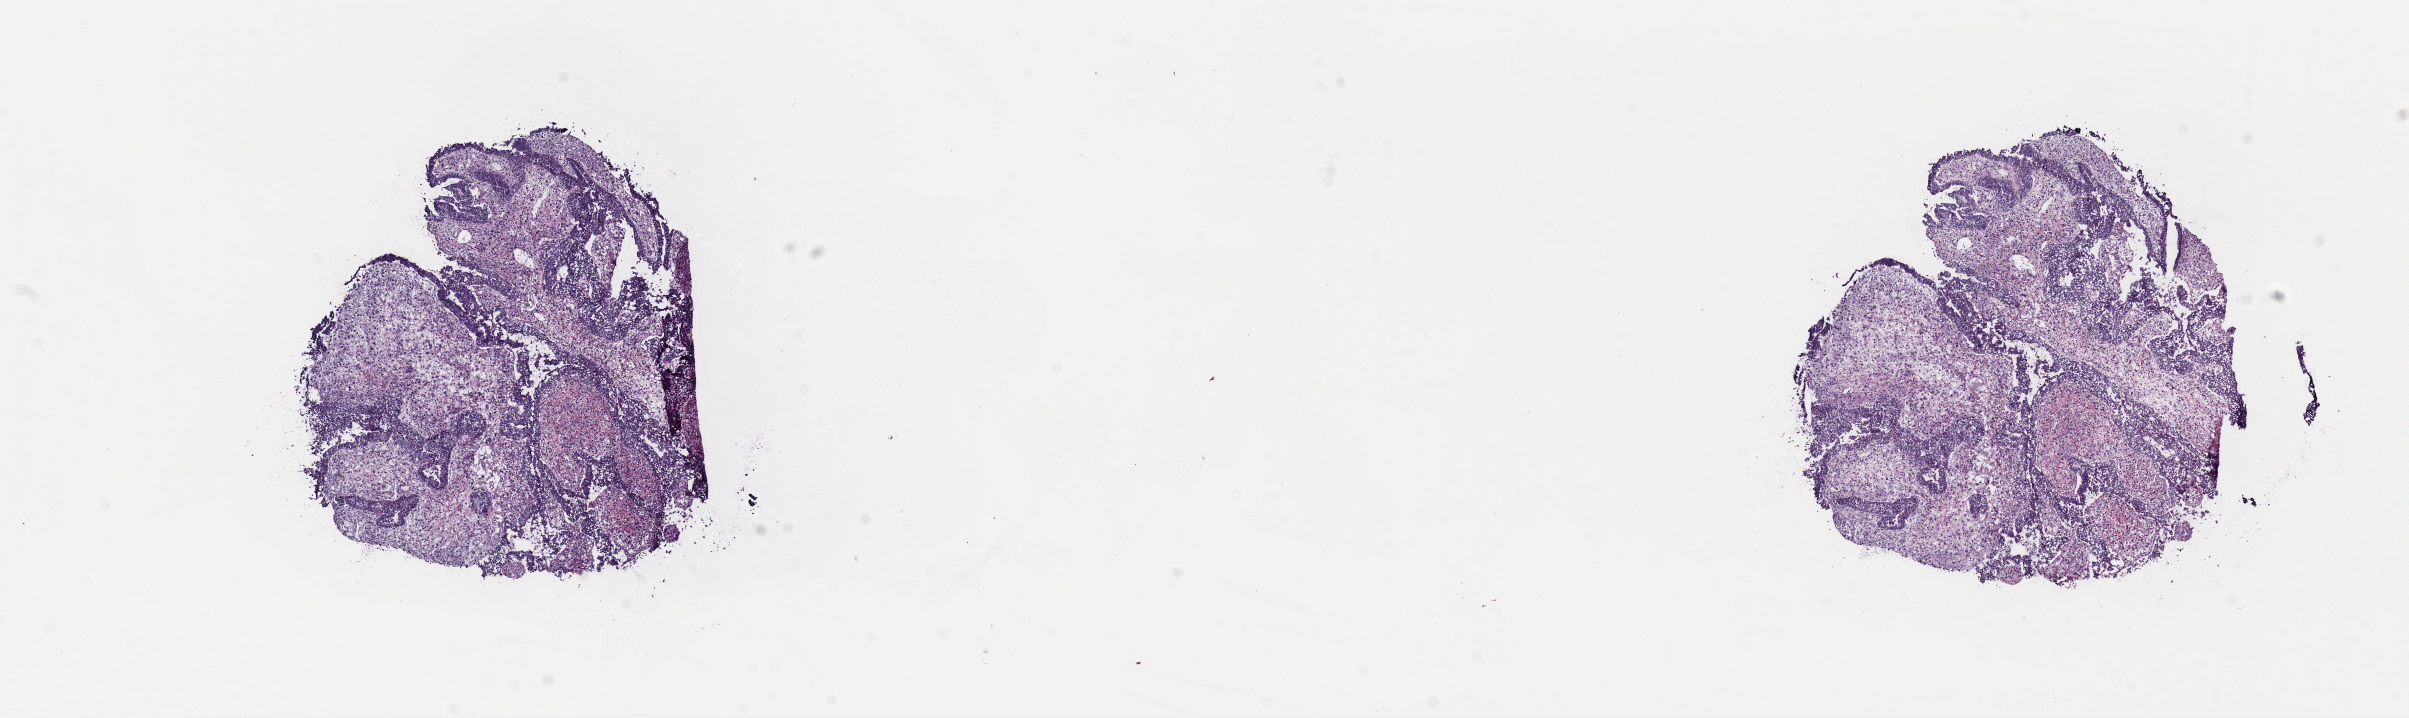
Digitized H&E tissue section (whole slide), whole scanned area (about 19.0 x 5.7 mm, slide scanned at 40x) shown as a low-resolution overview, frozen section from the top of the tissue portion, sample: primary tumour, uterus. Patient: female, age at initial diagnosis 73 years. Slide review estimates, as recorded: tumour cells 100%, tumour nuclei 85%, normal cells 0%, stromal cells 0%, necrosis 0%. Infiltration values recorded for this section: lymphocyte infiltration 2%, monocyte infiltration 0%, neutrophil infiltration 0%.
* lymph nodes positive (case pathology): 0 of 14 examined
* histologic diagnosis: Carcinosarcoma, NOS
* FIGO stage: IB